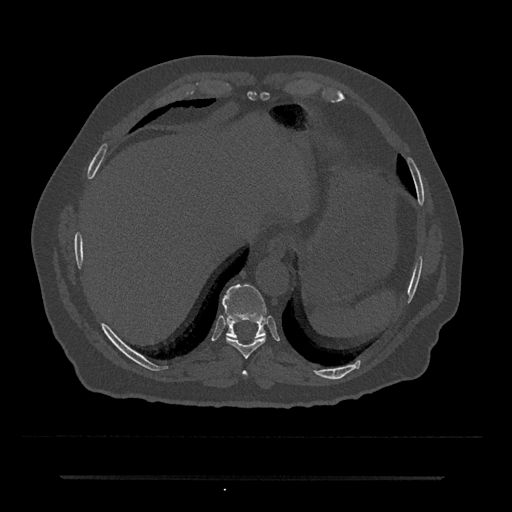
CT including the spine, one axial slice; reconstruction kernel Br40s/3; bone window (W 1800 / L 400 HU); 512 × 512 image matrix, field of view 437 × 437 mm. Male patient, age 69 years. Case-level facts recorded for this patient, not image findings: primary cancer: prostate.
Structures marked on this image (semi-automatic segmentation, software-assisted and operator-edited):
- T10 vertebra: box from (x=222, y=284) to (x=267, y=338) px
- T8 vertebra: (x=242, y=371)–(x=248, y=377)
- T9 vertebra: (x=226, y=336)–(x=266, y=359)